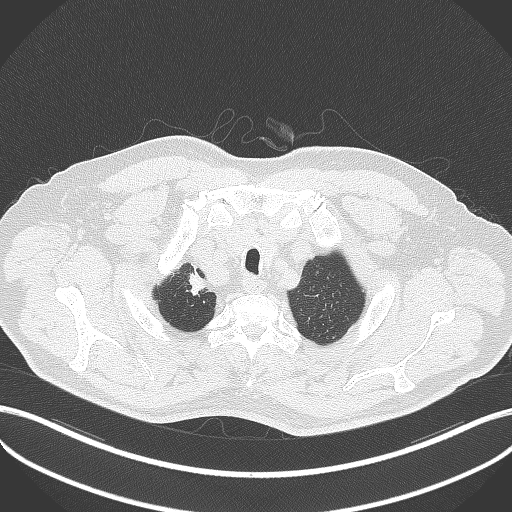
Chest CT, one axial slice; position 348 of 411 along the scan axis; reconstruction kernel B70f; 120 kVp; lung window (W 1500 / L -600 HU); 1 mm slice thickness; 512 × 512 image matrix, field of view 400 × 400 mm. Male patient, age 60 years. From the clinical record (not read from this slice): clinical TNM (as recorded): T1b N1 M0.
Structures marked on this image (bounding box drawn by a radiologist):
- lung tumour (recorded histology: squamous cell carcinoma): bounding box [x1, y1, x2, y2] px = [185, 268, 207, 296]